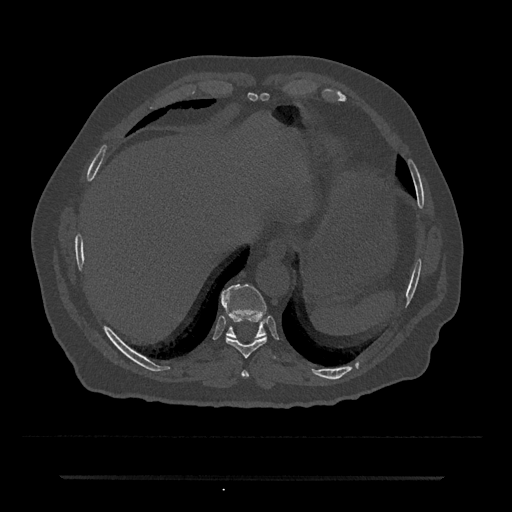
CT including the spine, one axial slice; slice 262 of 797 in the series (ordered by position); bone window (W 1800 / L 400 HU); 512 × 512 image matrix, field of view 437 × 437 mm. Patient: male, 69 years. Case-level facts recorded for this patient, not image findings: primary cancer: prostate.
Structures marked on this image (semi-automatic segmentation, software-assisted and operator-edited):
- T10 vertebra: bounding box [x1, y1, x2, y2] px = [221, 284, 267, 338]
- T8 vertebra: [241, 370, 249, 378]
- T9 vertebra: [226, 336, 276, 358]